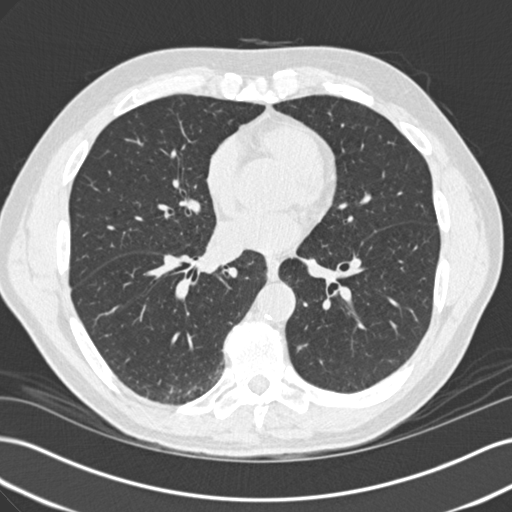
Axial slice from a low-dose chest CT screening exam; baseline annual screen; lung window (W 1500 / L -600 HU); standard (soft-tissue) reconstruction kernel (B30f). Male, age 64 years at enrolment.
Expert reader's lesion annotation, bounding box (x1, y1, x2, y2) in pixels: (282, 331, 316, 371). Screening reader's record for this exam: no non-calcified nodule ≥4 mm recorded. Official screen result: negative screen, minor abnormalities not suspicious for lung cancer. Lung cancer was diagnosed 844 days after this screen (after the third annual screen): adenocarcinoma with mixed subtypes, left lower lobe, well differentiated (G1), stage IA (AJCC 6th edition), 7 mm at pathology.